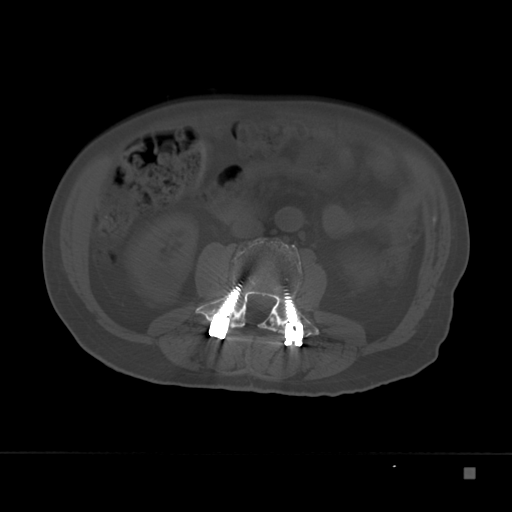
CT including the spine, one axial slice; slice 72 of 332 in the series (ordered by position); reconstruction kernel Br40s; bone window (W 1800 / L 400 HU); 1.5 mm slice thickness; 512 × 512 image matrix, field of view 389 × 389 mm. Male patient, age 72 years. Case-level facts recorded for this patient, not image findings: primary cancer: skeletal.
Structures marked on this image (semi-automatic segmentation, software-assisted and operator-edited):
- L2 vertebra: bounding box [x1, y1, x2, y2] px = [269, 318, 276, 325]
- L3 vertebra: [195, 237, 319, 337]